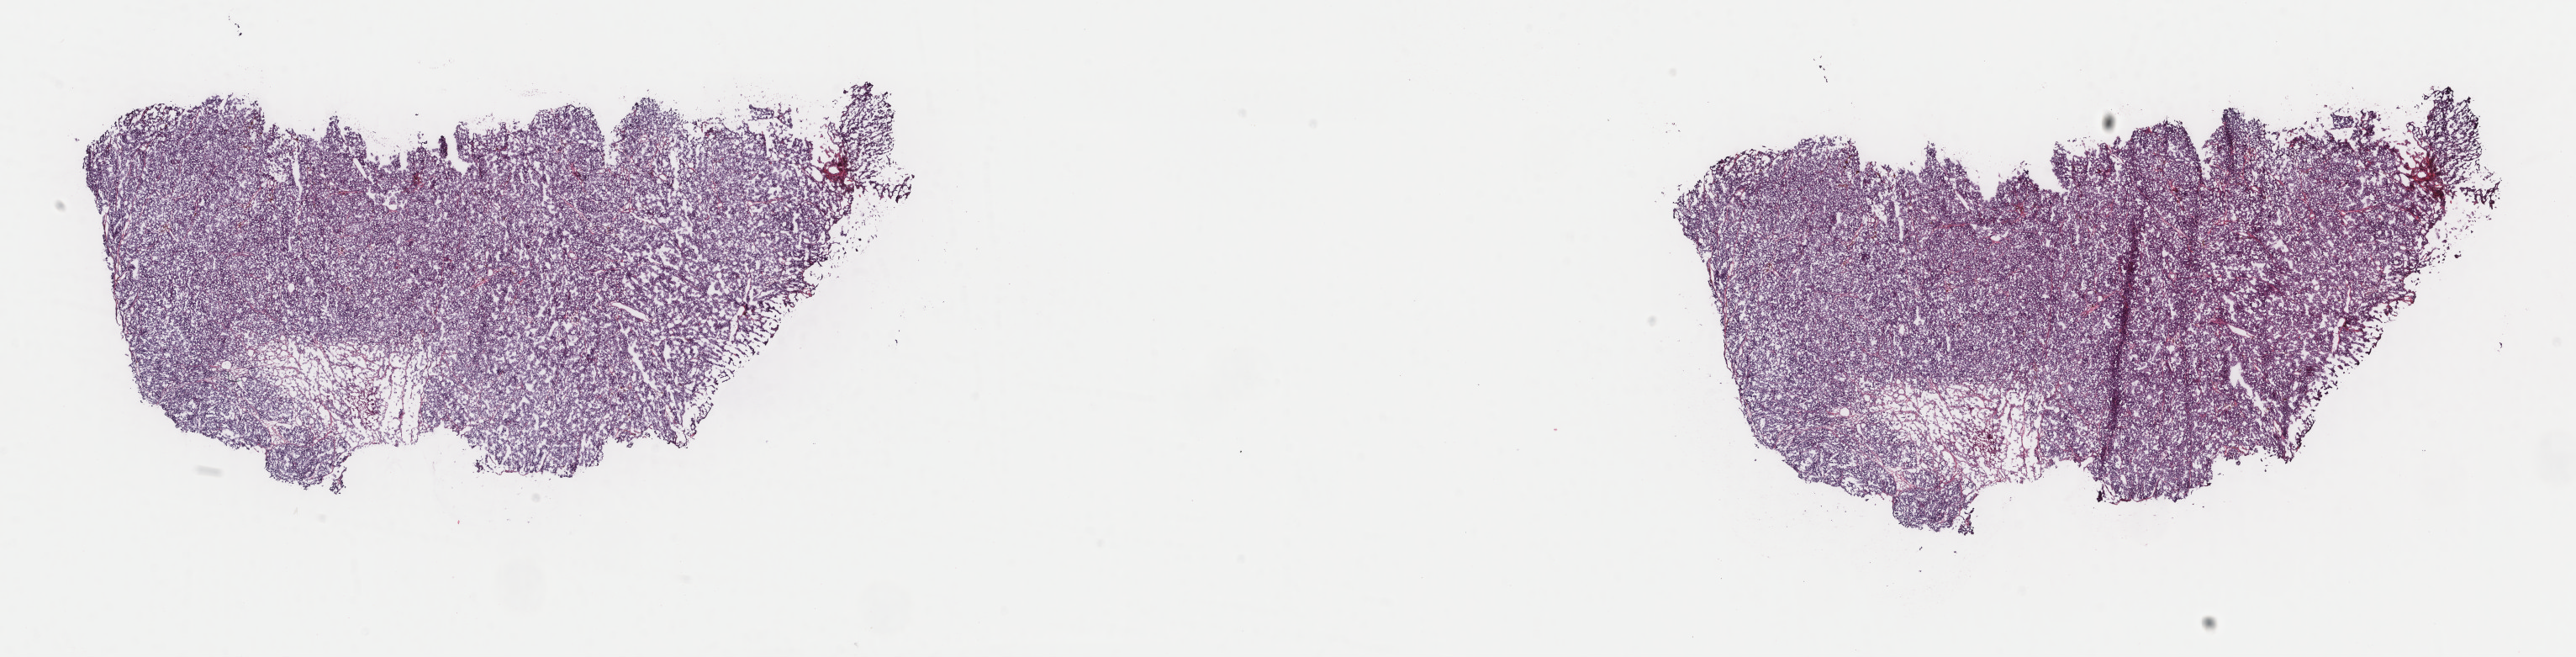
Digitized H&E-stained tissue section (whole slide) — whole scanned area (about 24.3 x 6.2 mm, slide scanned at 40x) shown as a low-resolution overview; frozen section; primary tumour sample from the skin. Female, age 76 years at initial diagnosis. Slide review estimates, as recorded: tumour cells 100%, tumour nuclei 98%, normal cells 0%, stromal cells 0%, necrosis 0%. Inflammatory infiltration, as recorded: lymphocyte infiltration 0%, monocyte infiltration 0%, neutrophil infiltration 0%.
AJCC pathologic stage: IIC. Histologic diagnosis: Nodular melanoma.